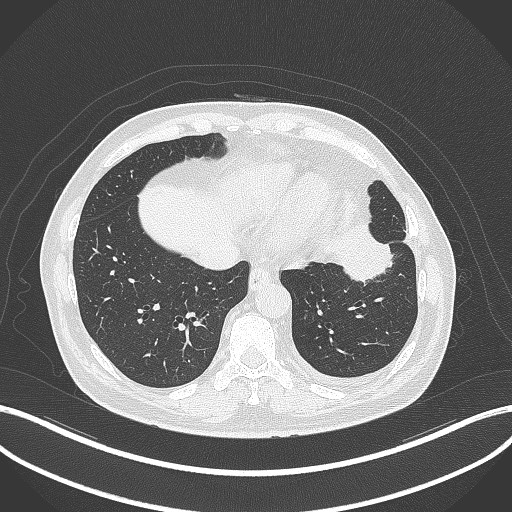
Chest CT, one axial slice. Slice 96 of 230 in the series (ordered by position). 120 kVp. Lung window (W 1500 / L -600 HU). 1 mm slice thickness. 512 × 512 image matrix, field of view 400 × 400 mm. Male patient, age 68 years. From the clinical record (not read from this slice): clinical TNM (as recorded): T2b N0 M0.
Structures marked on this image (rectangle marked by the reading radiologist):
- lung tumour (recorded histology: squamous cell carcinoma): bounding box (x1, y1, x2, y2) in pixels: (326, 221, 399, 286)